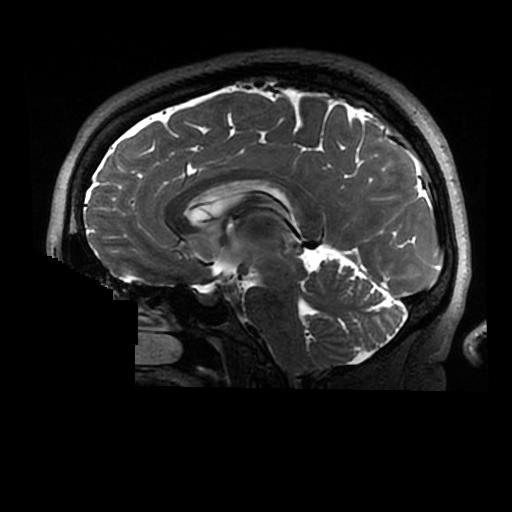
Brain MRI from a brain-tumour surgery series, one sagittal slice. Slice 150 of 320 in the series (ordered by position). 0.6 mm slice thickness. 512 × 512 image matrix, field of view 240 × 240 mm. Case-level facts recorded for this patient, not image findings: histopathology: Astrocytoma; WHO grade: 2; IDH mutation: yes.
Structures marked on this image (outlined manually by an expert reader):
- tumour: bounding box <277,208,295,242> (left, top, right, bottom; pixels)